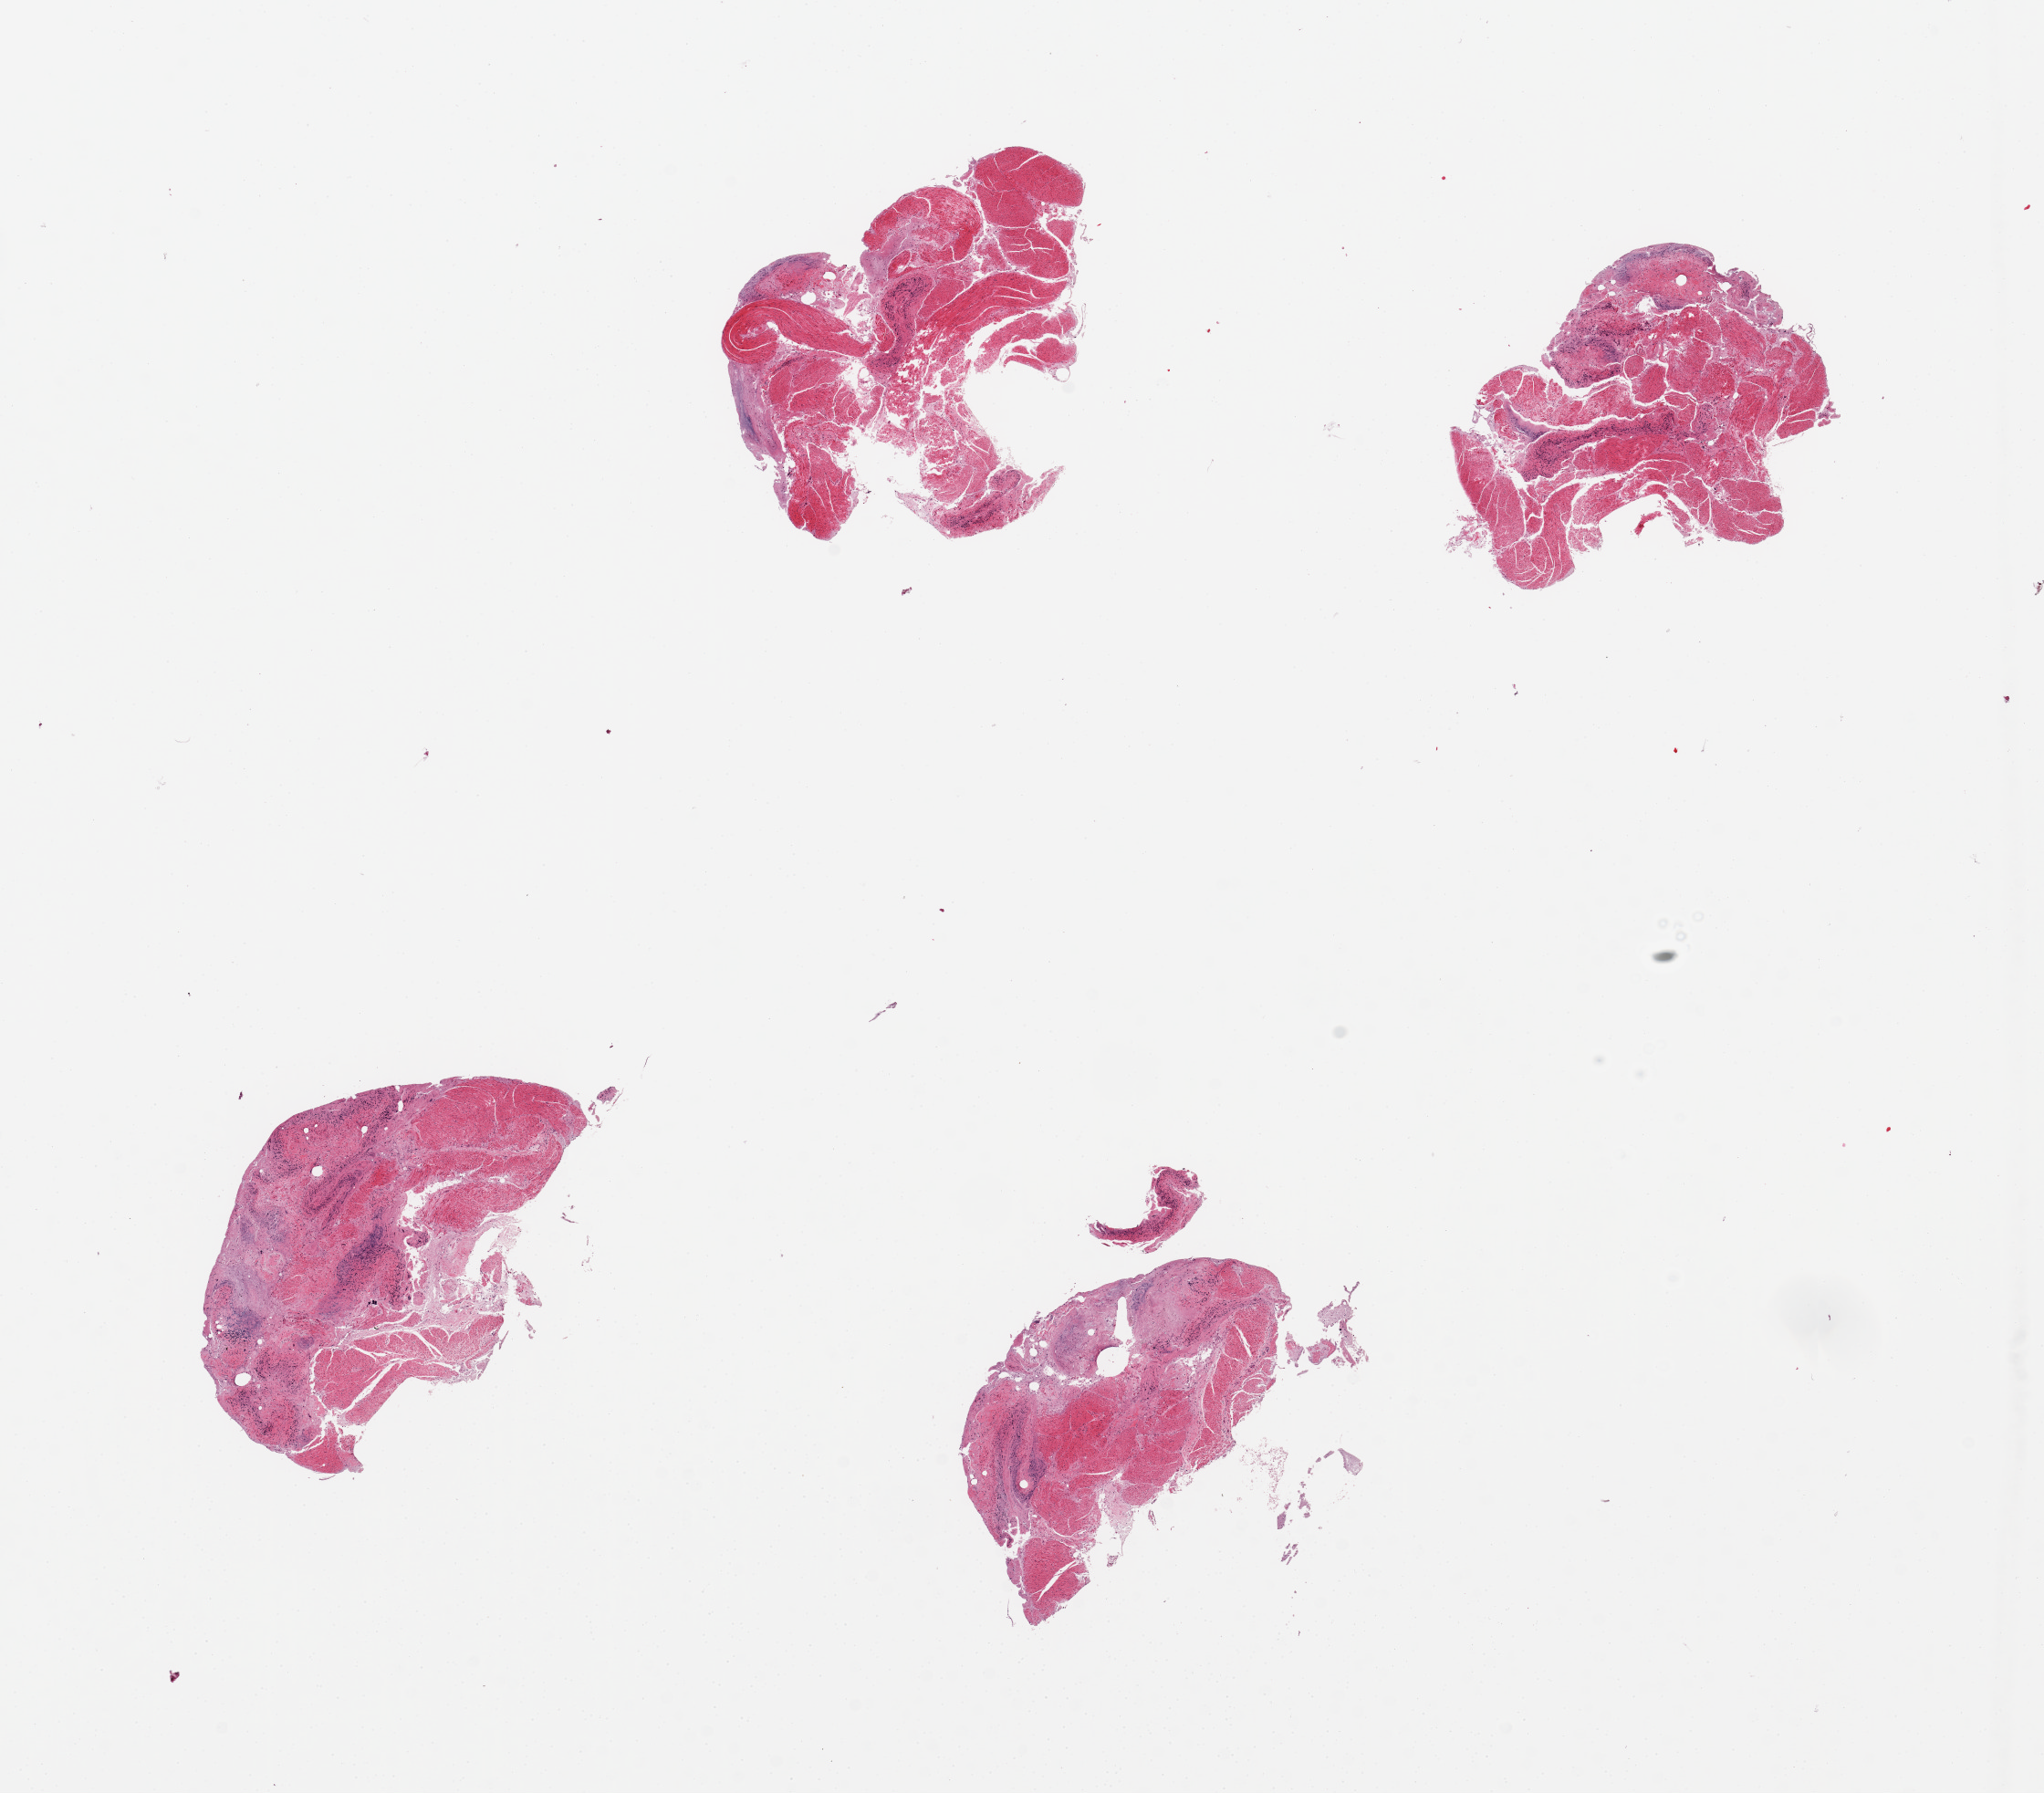
H&E whole-slide image, shown as a low-resolution overview of the whole scanned area (about 17.7 x 15.5 mm, acquisition: 20x scan); PAXgene-fixed, paraffin-embedded tissue; section of ileum (target tissue); donor tissue sample. Donor: female.
Pathologist's review note for this sample: 4 pieces, badly autolyzed. About ~10-15% lympohoid elements.